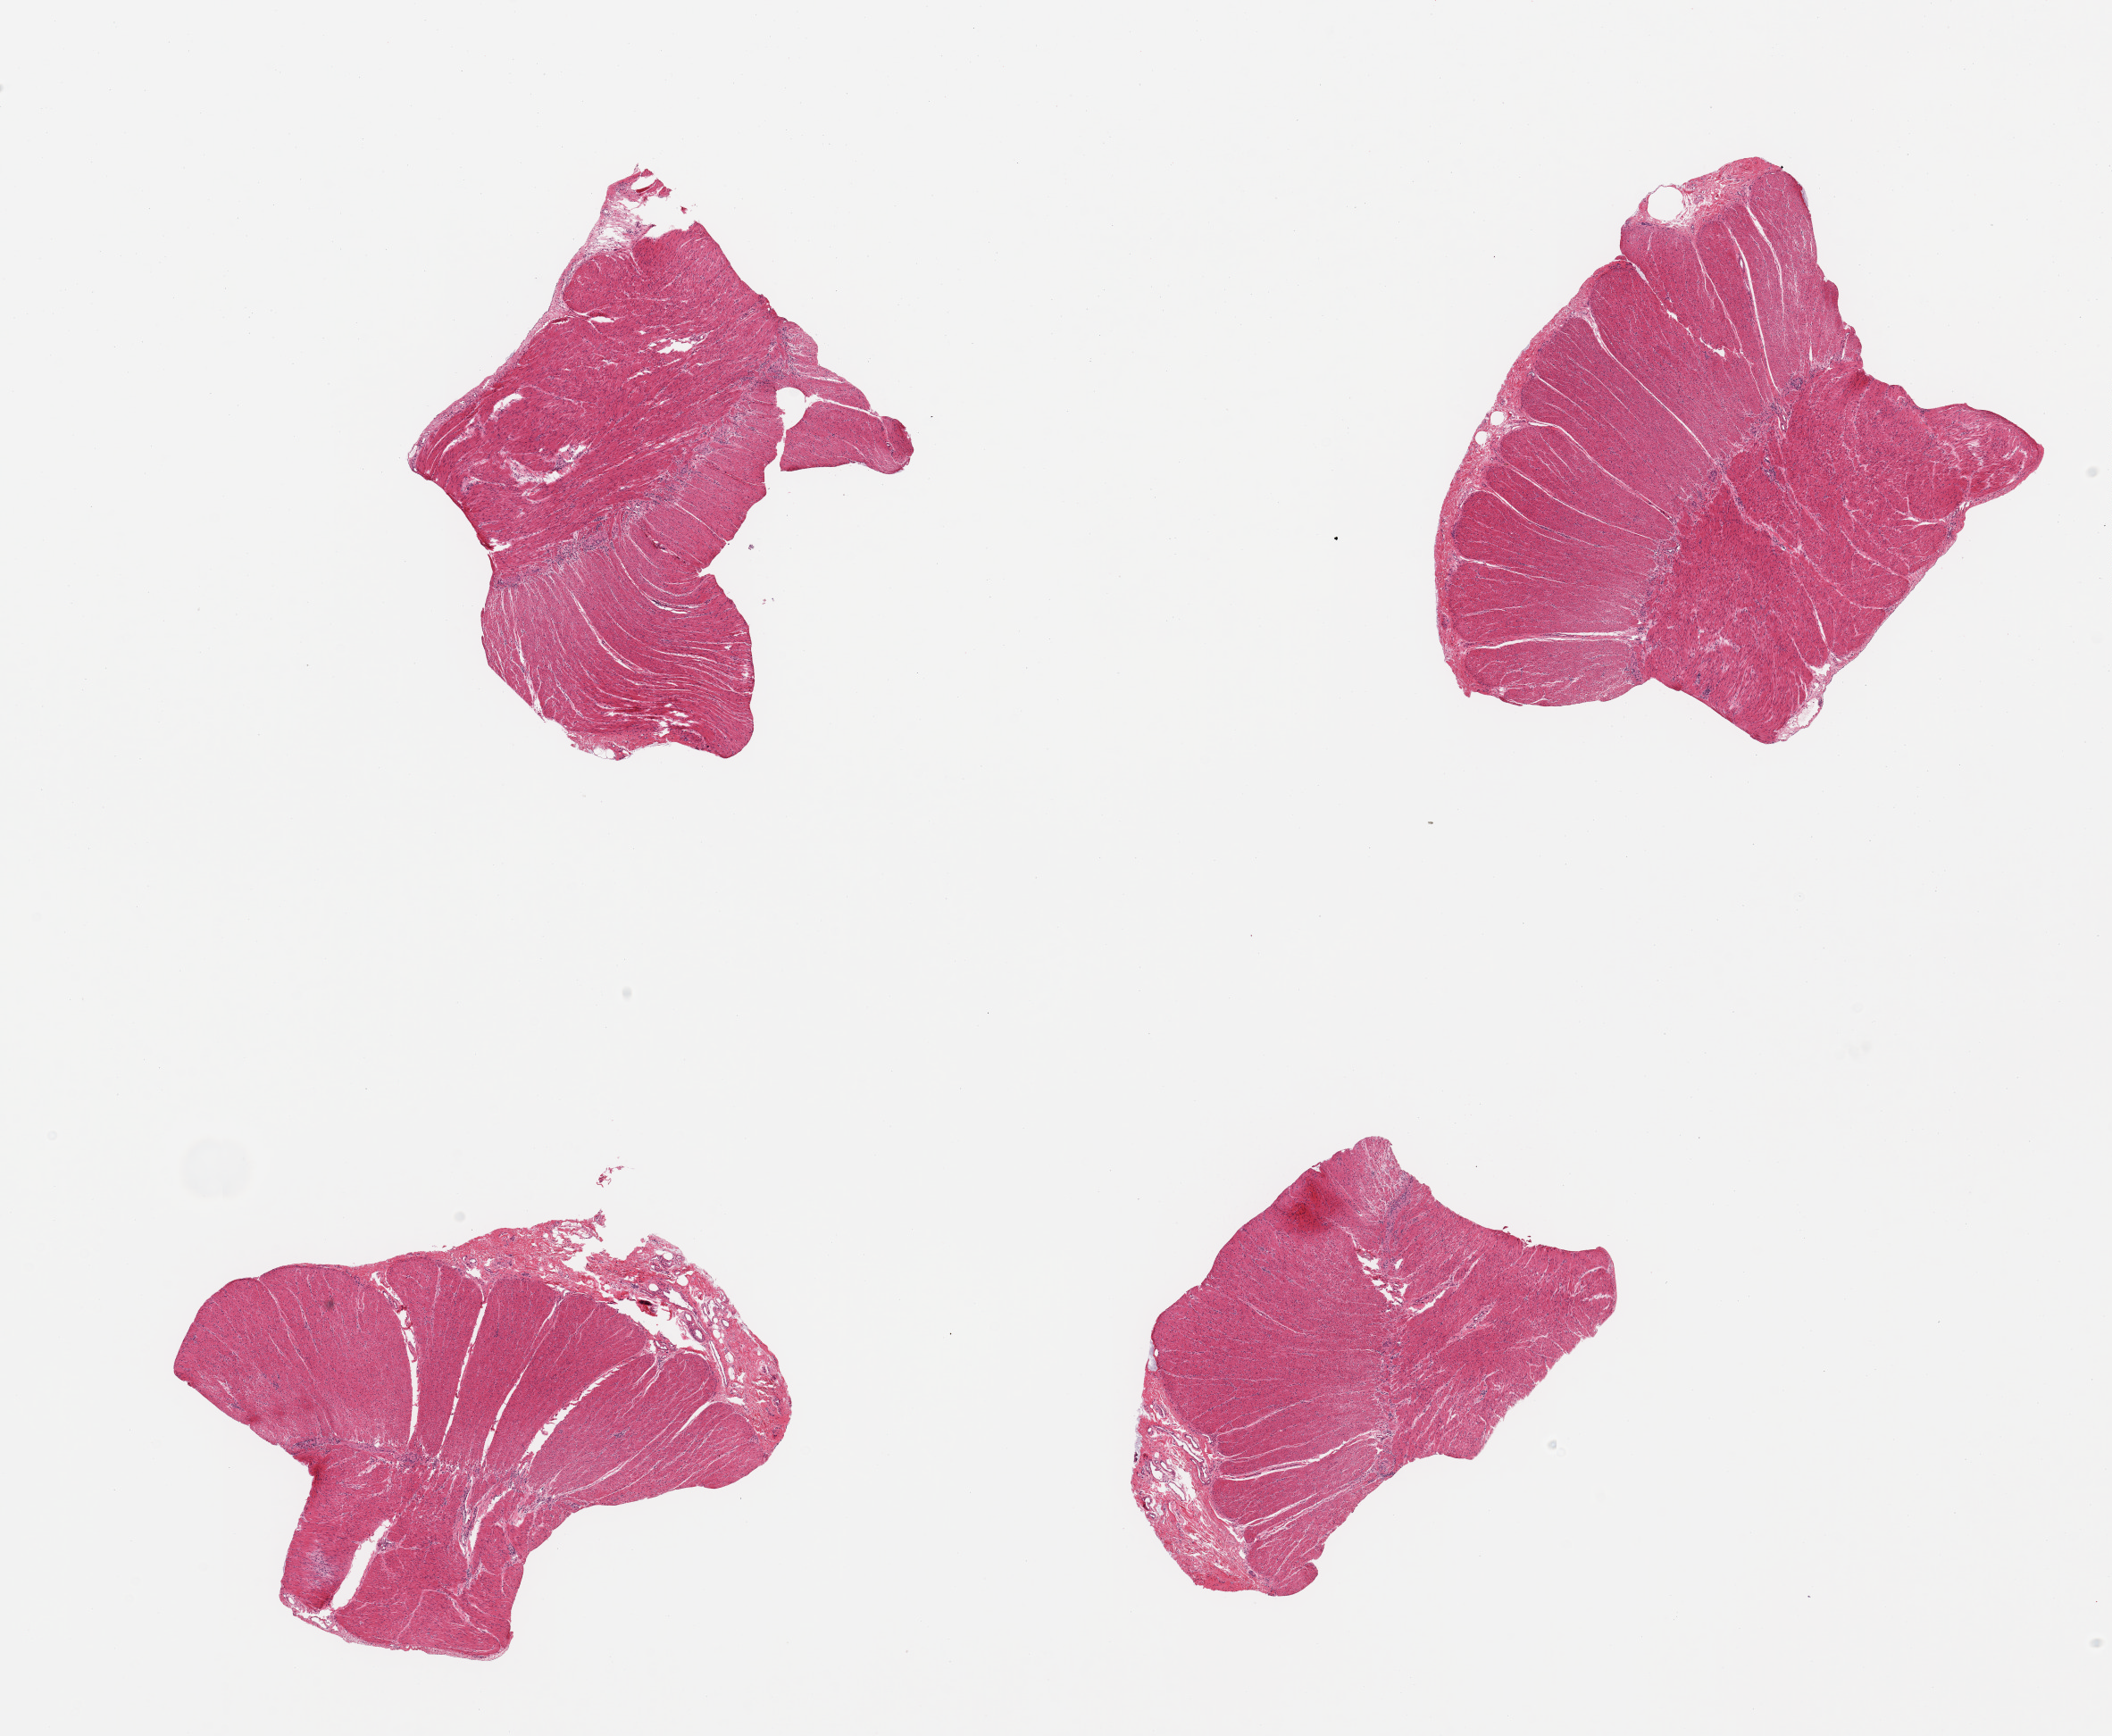
Digitized hematoxylin and eosin (H&E)-stained section, shown as a low-resolution overview of the whole scanned area (about 18.7 x 15.4 mm); PAXgene-fixed, paraffin-embedded tissue; target tissue: sigmoid colon; donor tissue sample.
Reviewer comment on this tissue sample: 4 pieces, target muscularis.